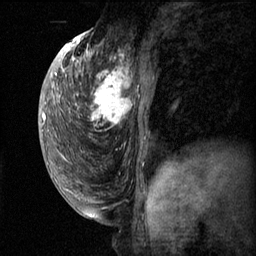
Breast MRI (dynamic contrast-enhanced), one sagittal slice; position 29 of 60 along the scan axis; dynamic contrast-enhanced series, image 2 of 3 at this slice position (ordered by acquisition); 1.5 T; TE 4.2 ms, TR 11.1 ms; 256 × 256 image matrix, field of view 180 × 180 mm. Patient: female, 50 years.
Structures marked on this image (semi-automatic segmentation, software-assisted and operator-edited):
- analysis volume of interest (the breast-tissue region the enhancement analysis was run in; not a lesion): bounding box (x1, y1, x2, y2) in pixels: (82, 56, 154, 143)
- tumour enhancement mask (voxels above the 70 % enhancement threshold inside the analysis volume of interest): (82, 56, 132, 125)